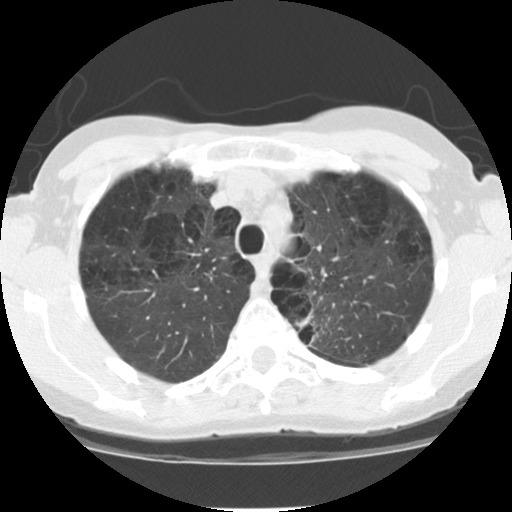
Low-dose screening chest CT, one axial slice. Slice 91 of 116 in the series (ordered by position). 120 kVp. Lung window (W 1500 / L -600 HU). 2.5 mm slice thickness. 512 × 512 image matrix, field of view 300 × 300 mm.
Annotated regions visible in this slice (expert manual segmentation):
- lesion 1 (tumor, upper lobe of left lung): bounding box <296,311,323,346> (left, top, right, bottom; pixels)